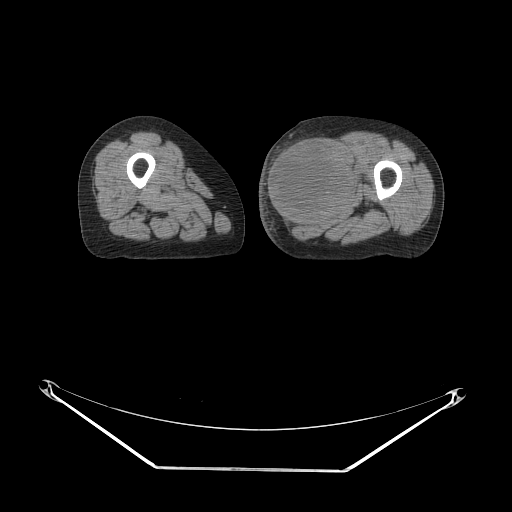
CT of an extremity soft-tissue mass (from a PET/CT study), one axial slice. Position 30 of 91 along the scan axis. 140 kVp. Soft-tissue window (W 400 / L 40 HU). 512 × 512 image matrix, field of view 500 × 500 mm. Female patient. Case-level facts recorded for this patient, not image findings: histological type: pleomorphic leiomyosarcoma; grade: high; site of the primary tumour: left thigh.
Outlined on this slice (expert contour drawn on MRI and transferred to this co-registered scan by the dataset authors):
- gross tumour volume including surrounding oedema: bounding box [x1, y1, x2, y2] px = [265, 135, 355, 227]
- gross tumour volume (mass): [265, 135, 355, 225]